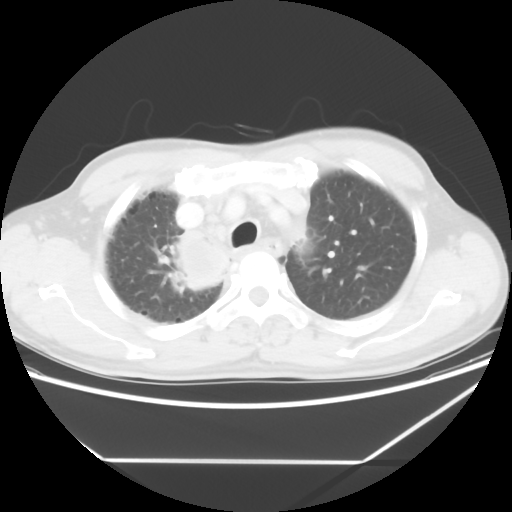
Chest CT, one axial slice; slice 48 of 60 in the series (ordered by position); lung window (W 1500 / L -600 HU); 5 mm slice thickness; 512 × 512 image matrix, field of view 367 × 367 mm. Patient: male, 58 years. Case-level facts recorded for this patient, not image findings: clinical TNM (as recorded): T2 N2 M0.
Structures marked on this image (rectangle marked by the reading radiologist):
- lung tumour (recorded histology: squamous cell carcinoma): bounding box (x1, y1, x2, y2) in pixels: (154, 216, 251, 303)